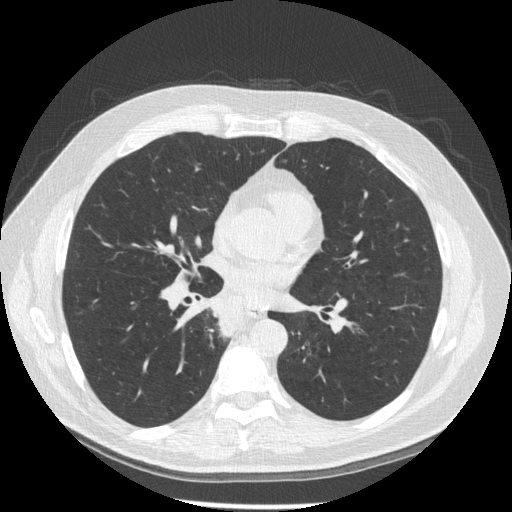
Low-dose screening chest CT, one axial slice. Slice 93 of 181 in the series (ordered by position). Reconstruction kernel STANDARD. Lung window (W 1500 / L -600 HU). 1.25 mm slice thickness. 512 × 512 image matrix, field of view 370 × 370 mm.
Outlined on this slice (expert manual segmentation):
- lesion 1 (tumor, lower lobe of right lung): bounding box [x1, y1, x2, y2] px = [211, 300, 242, 337]